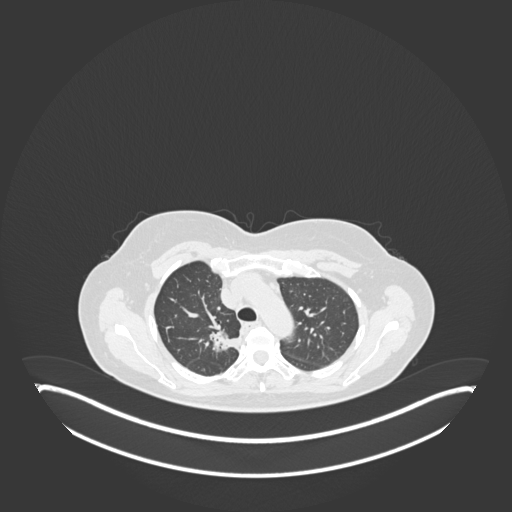
Chest CT, one axial slice; slice 132 of 181 in the series (ordered by position); reconstruction kernel B30f; 120 kVp; lung window (W 1500 / L -600 HU); 512 × 512 image matrix, field of view 500 × 500 mm. Patient: female, 65 years. From the clinical record (not read from this slice): clinical TNM (as recorded): T1b N0 M0.
Annotated regions visible in this slice (bounding box drawn by a radiologist):
- lung tumour (recorded histology: adenocarcinoma): bounding box (x1, y1, x2, y2) in pixels: (206, 328, 240, 354)